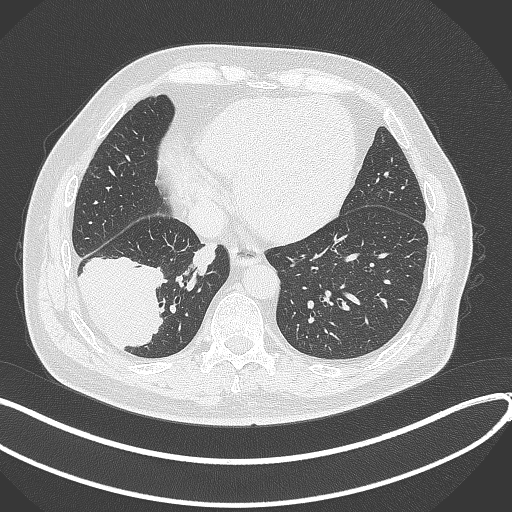
Chest CT, one axial slice. Slice 104 of 360 in the series (ordered by position). Reconstruction kernel B70f. 120 kVp. Lung window (W 1500 / L -600 HU). 1 mm slice thickness. 512 × 512 image matrix. Patient: male, 59 years.
Structures marked on this image (bounding box drawn by a radiologist):
- lung tumour (recorded histology: adenocarcinoma): bounding box [x1, y1, x2, y2] px = [76, 251, 167, 350]